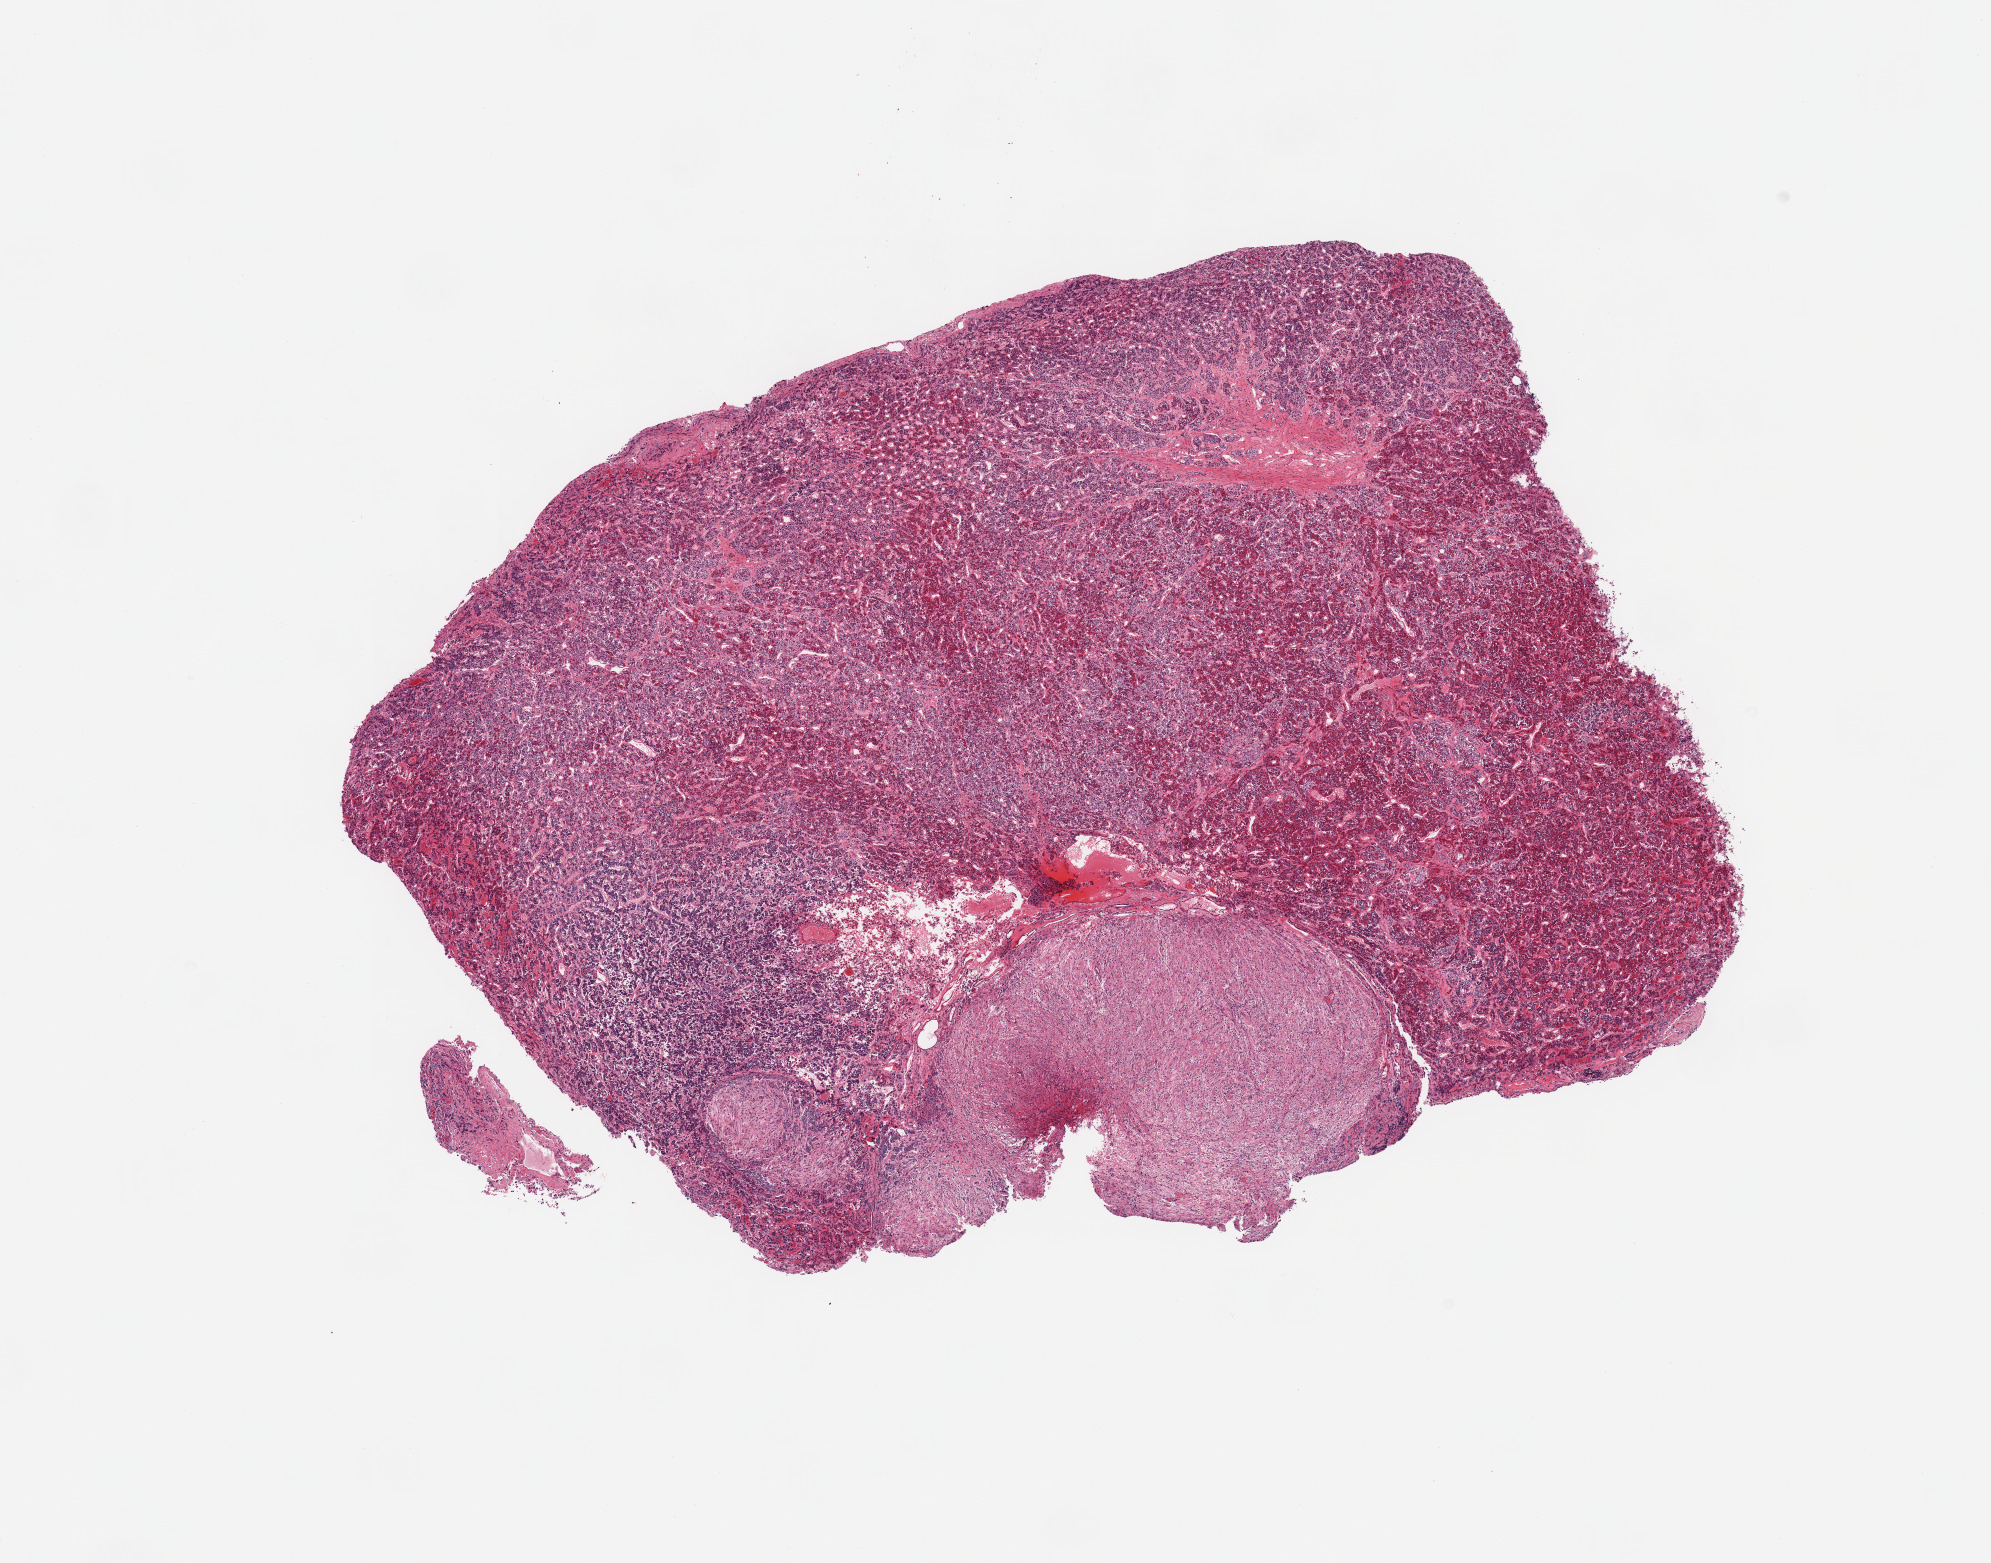
Whole-slide image, haematoxylin and eosin stain, whole scanned area (about 15.8 x 12.4 mm) shown as a low-resolution overview, PAXgene-fixed, paraffin-embedded tissue, sampled site (target tissue): pituitary, donor tissue sample. Male donor.
- reviewer comment on this tissue sample: 1 piece; adenohypophysis and neurohypophysis present